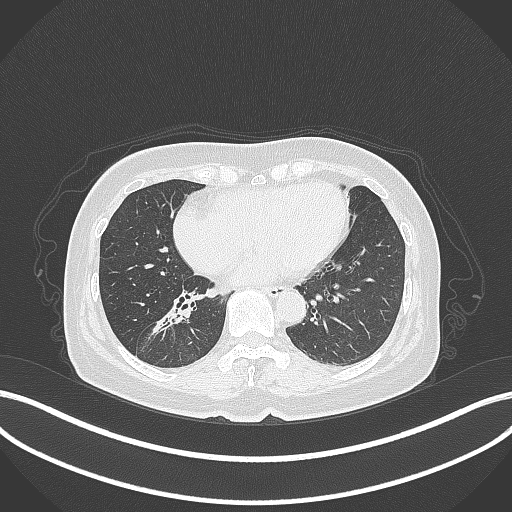
Chest CT, one axial slice; position 152 of 429 along the scan axis; reconstruction kernel B70f; 120 kVp; lung window (W 1500 / L -600 HU); 1 mm slice thickness; 512 × 512 image matrix, field of view 400 × 400 mm. Female patient, age 67 years. From the clinical record (not read from this slice): clinical TNM (as recorded): T1c N1 M0; histopathological grade: G2-3.
Outlined on this slice (bounding box drawn by a radiologist):
- lung tumour (recorded histology: adenocarcinoma): bounding box <146,294,197,342> (left, top, right, bottom; pixels)